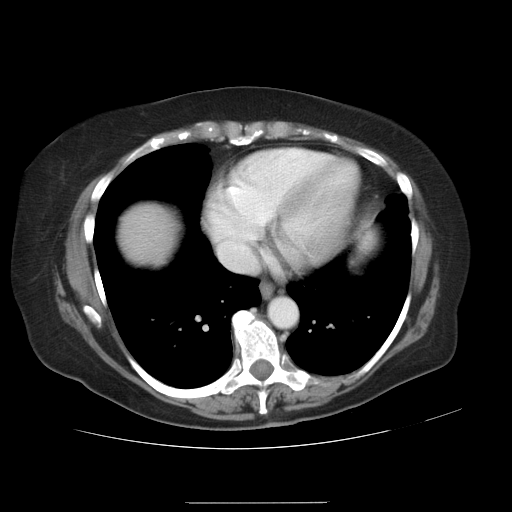
Contrast-enhanced abdominal CT, one axial slice. Position 29 of 32 along the scan axis. Reconstruction kernel STANDARD. 120 kVp. Soft-tissue window (W 400 / L 40 HU). 512 × 512 image matrix, field of view 386 × 386 mm. Female patient, age 65 years. Case-level facts recorded for this patient, not image findings: diagnosis: colorectal cancer liver metastases, imaged before liver resection; multiple liver metastases: yes; largest metastasis: 1.7 cm; disease in both lobes: no.
Annotated regions visible in this slice (manually delineated by an expert):
- liver: box from (x=121, y=205) to (x=174, y=261) px
- planned liver remnant (the part of the liver to remain after resection): (x=120, y=206)–(x=174, y=260)